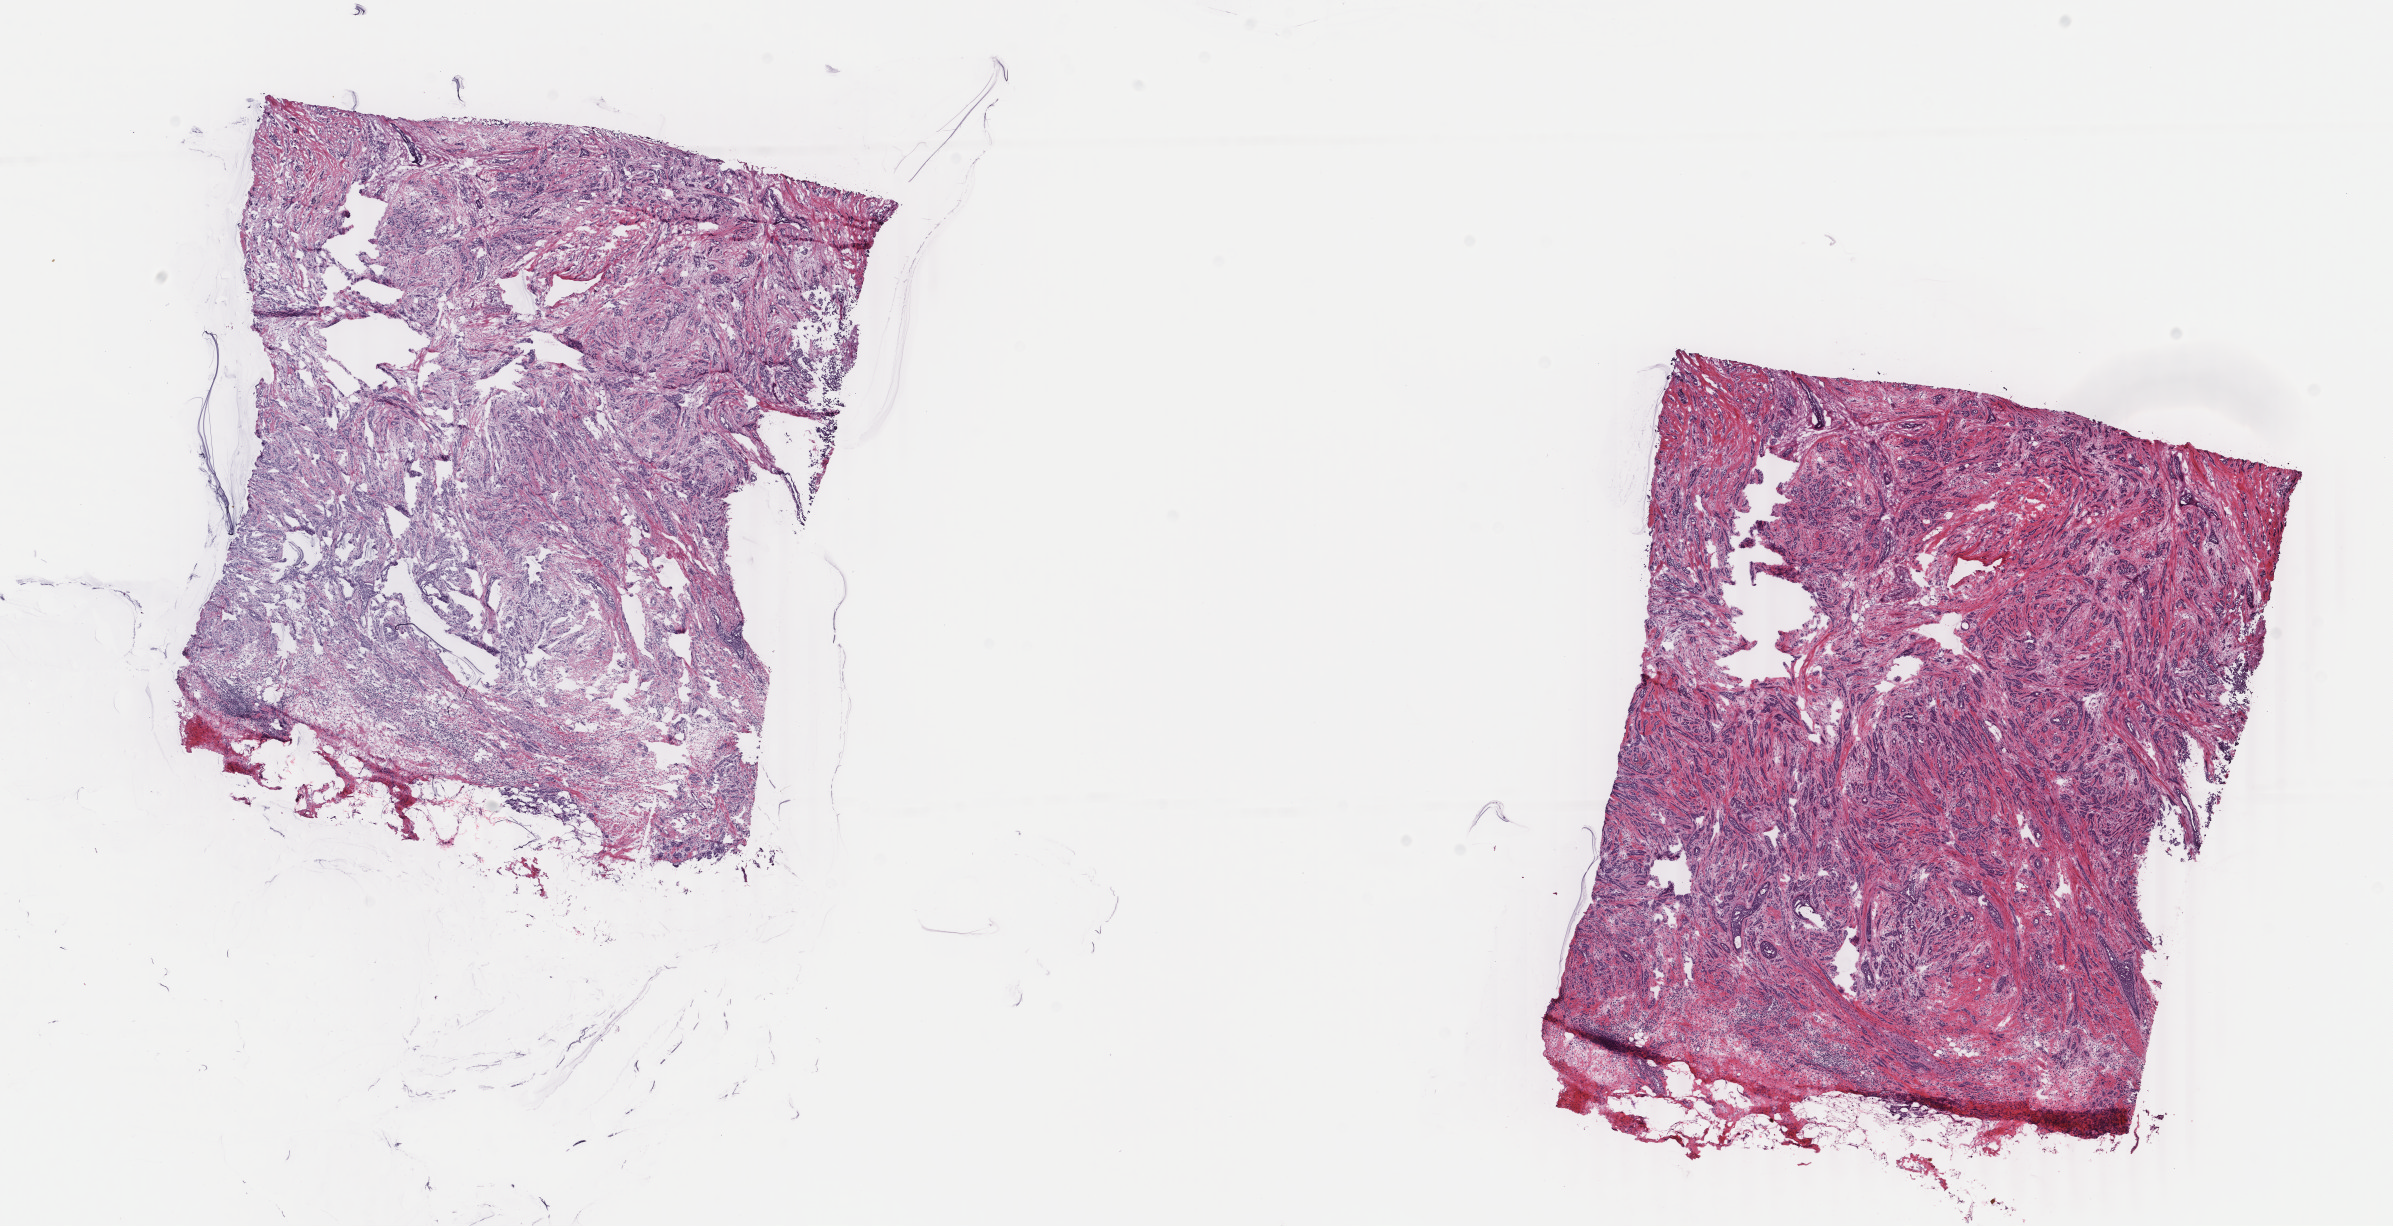
Digitized Hematoxylin and eosin (H&E) stained tissue section (whole slide), whole scanned area (about 19.0 x 9.8 mm) shown as a low-resolution overview; frozen section from the top of the tissue portion; sample: primary tumour, breast. Female patient; age at initial diagnosis 38 years. Slide review estimates, as recorded: tumour cells 75%, tumour nuclei 75%, normal cells 2%, stromal cells 23%, necrosis 0%. Infiltration values recorded for this section: lymphocyte infiltration 4%, monocyte infiltration 1%, neutrophil infiltration 1%.
• lymph nodes positive (case pathology): 4 of 28 examined
• laterality: left
• TNM: T2 N2 M0
• AJCC pathologic stage: IIIA
• diagnosis: Infiltrating duct and lobular carcinoma